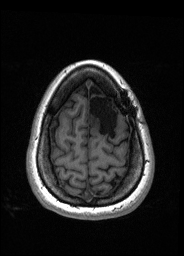
Pre-operative brain MRI before brain-tumour surgery, one axial slice. Position 40 of 176 along the scan axis. T1-weighted post-contrast. 1 mm slice thickness. 184 × 256 image matrix. Case-level facts recorded for this patient, not image findings: histopathology: Oligodendroglioma; WHO grade: 2; IDH mutation: yes.
Annotated regions visible in this slice (manually delineated by an expert):
- tumour: box from (x=88, y=112) to (x=100, y=128) px